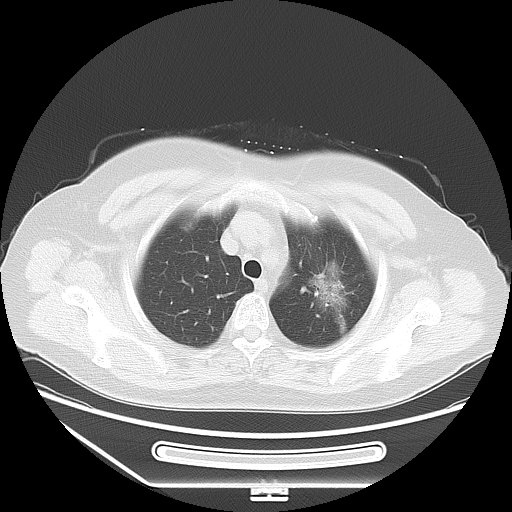
Chest CT, one axial slice; position 45 of 53 along the scan axis; reconstruction kernel LUNG; 120 kVp; lung window (W 1500 / L -600 HU); 512 × 512 image matrix. Female patient, age 66 years. Case-level facts recorded for this patient, not image findings: clinical TNM (as recorded): T2 N0 M0.
Structures marked on this image (bounding box drawn by a radiologist):
- lung tumour (recorded histology: adenocarcinoma): bounding box [x1, y1, x2, y2] px = [300, 258, 364, 329]